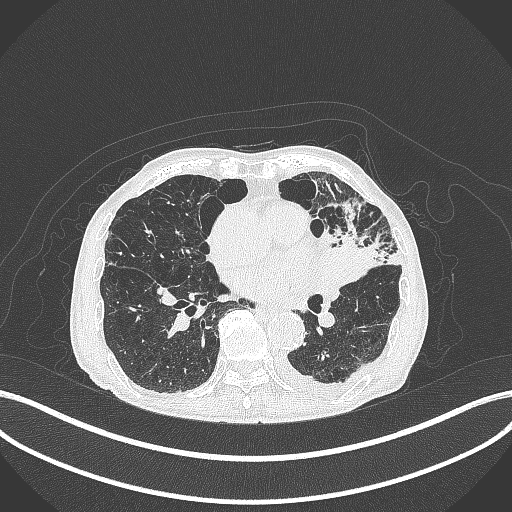
Chest CT, one axial slice; position 174 of 385 along the scan axis; 120 kVp; lung window (W 1500 / L -600 HU); 512 × 512 image matrix. Male patient, age 90 years or older. From the clinical record (not read from this slice): clinical TNM (as recorded): T2b N1 M0.
Structures marked on this image (rectangle marked by the reading radiologist):
- lung tumour (recorded histology: squamous cell carcinoma): bounding box [x1, y1, x2, y2] px = [316, 231, 378, 286]